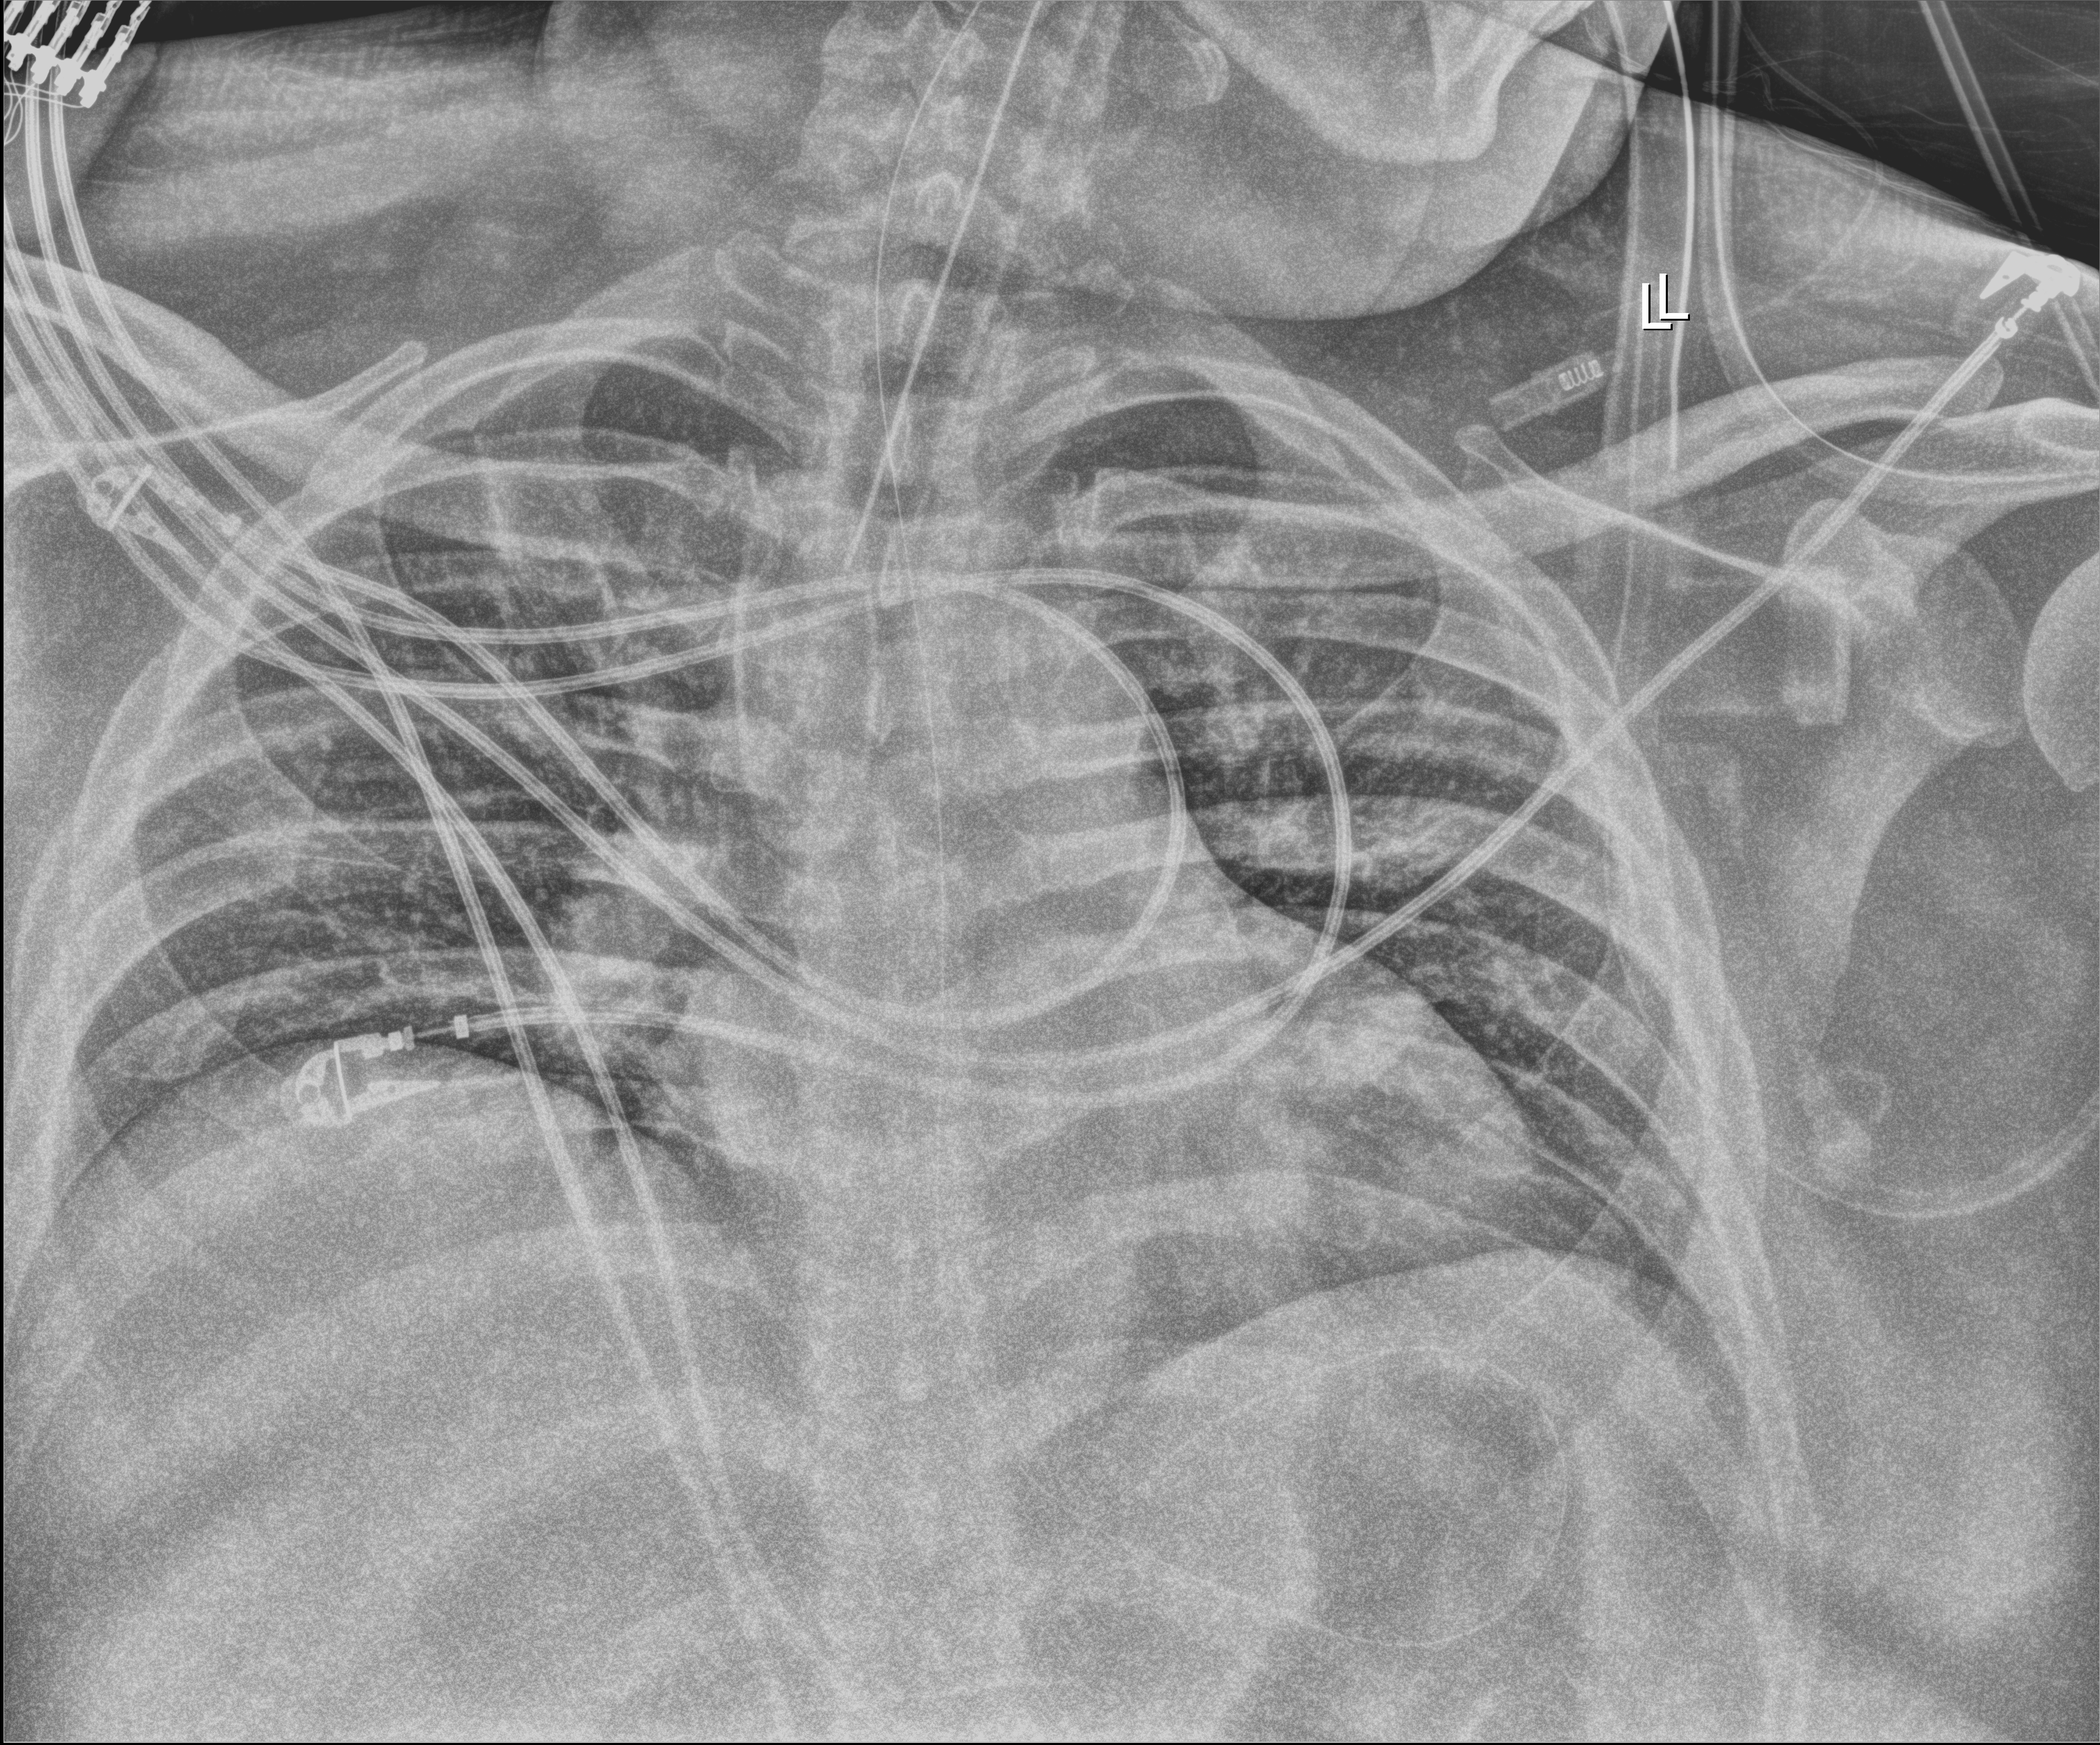
Bedside chest radiograph (digital radiography); anteroposterior (AP) projection. Patient hospitalised with COVID-19; male, aged 18–59 years.
Hospital-stay facts (about this admission, not read from this image; timing relative to this image not recorded): mechanically ventilated during this hospital stay: yes; admitted to intensive care during this hospital stay: yes; other chronic lung disease (admission record): yes.